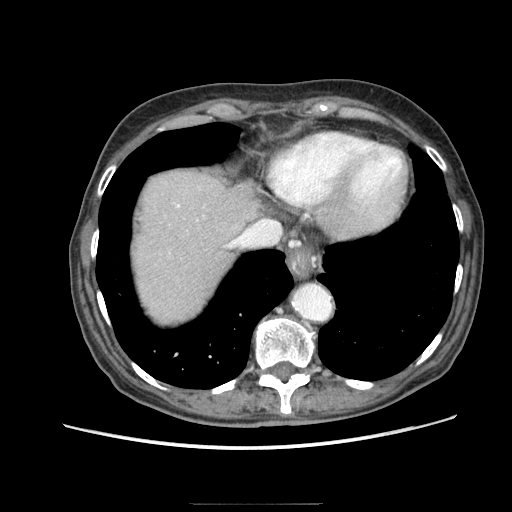
Contrast-enhanced abdominal CT (liver protocol), one axial slice; slice 73 of 83 in the series (ordered by position); reconstruction kernel STANDARD; soft-tissue window (W 400 / L 40 HU); 2.5 mm slice thickness; 512 × 512 image matrix, field of view 360 × 360 mm. From the clinical record (not read from this slice): diagnosis: hepatocellular carcinoma (patient treated with transarterial chemoembolisation; whether this scan precedes or follows treatment is not stated here); TNM stage (as recorded): Stage-I; Child-Pugh class: A.
Structures marked on this image (semi-automatic segmentation, software-assisted and operator-edited):
- liver parenchyma outside the tumour (the mass and vessels are separate outlines, so this box may not span the whole liver): bounding box [x1, y1, x2, y2] px = [134, 170, 259, 320]
- liver vessels: [177, 205, 232, 247]